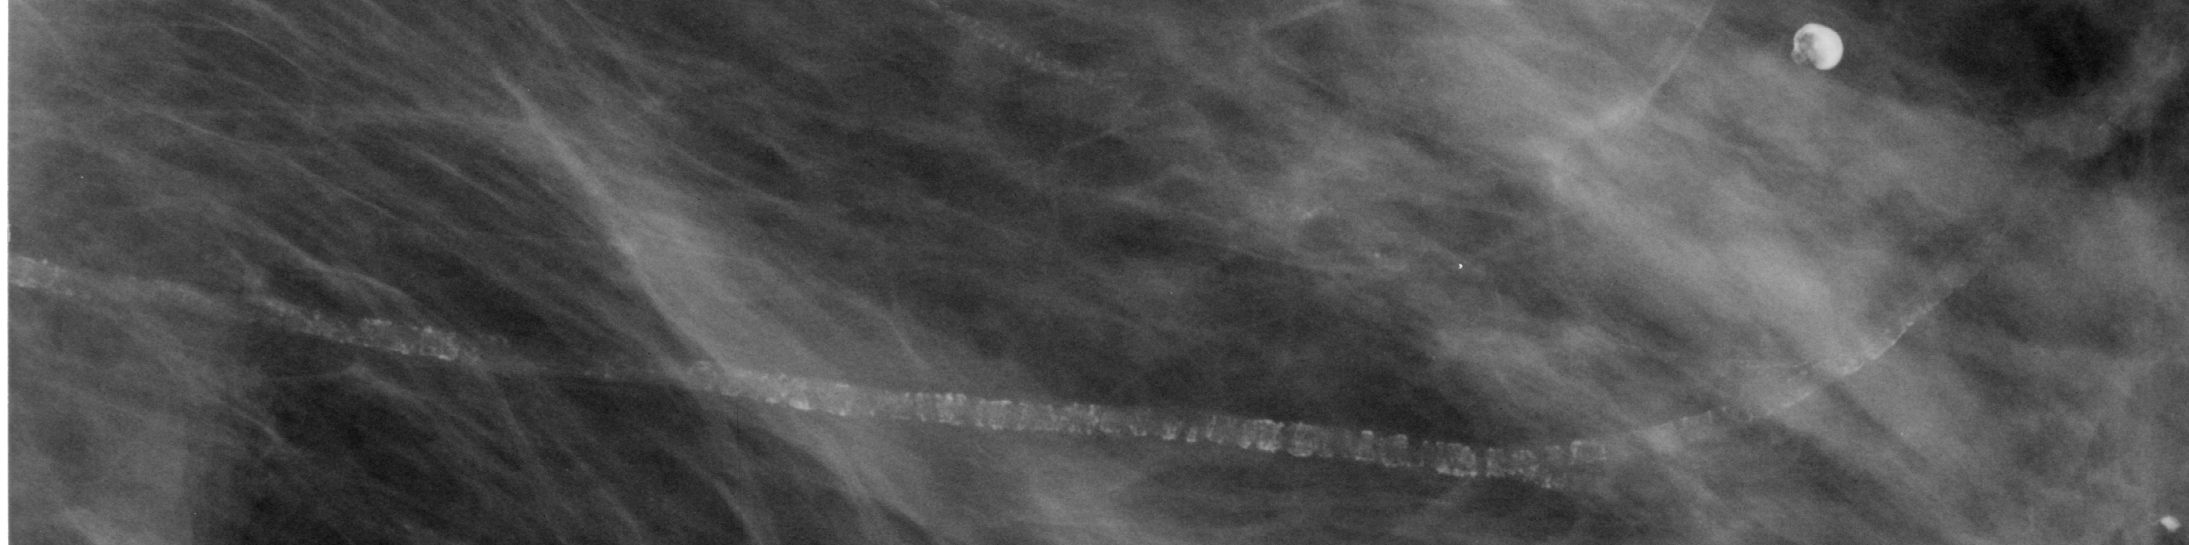
Region of interest cut from a scanned film mammogram (one marked finding); left breast; MLO view.
Calcifications, morphology vascular / coarse / lucent centered; BI-RADS assessment category 2; benign without callback (not worked up further).